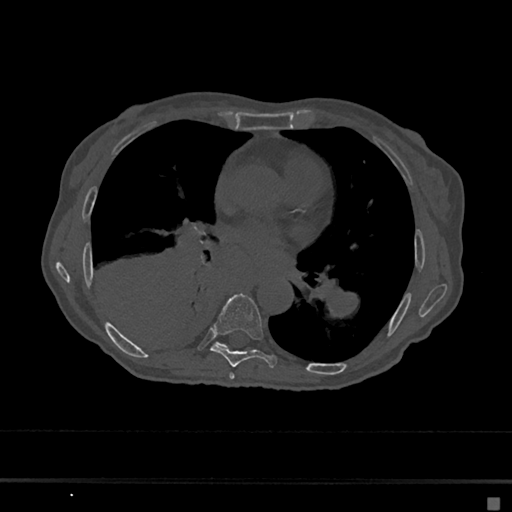
CT including the spine, one axial slice. Position 365 of 797 along the scan axis. Reconstruction kernel Br40s/3. Bone window (W 1800 / L 400 HU). 0.5 mm slice thickness. 512 × 512 image matrix. Female patient, age 68 years. Case-level facts recorded for this patient, not image findings: primary cancer: renal.
Outlined on this slice (semi-automatically segmented with operator editing):
- T6 vertebra: box from (x=229, y=372) to (x=235, y=379) px
- T7 vertebra: (x=210, y=293)–(x=277, y=368)
- T8 vertebra: (x=217, y=343)–(x=227, y=347)